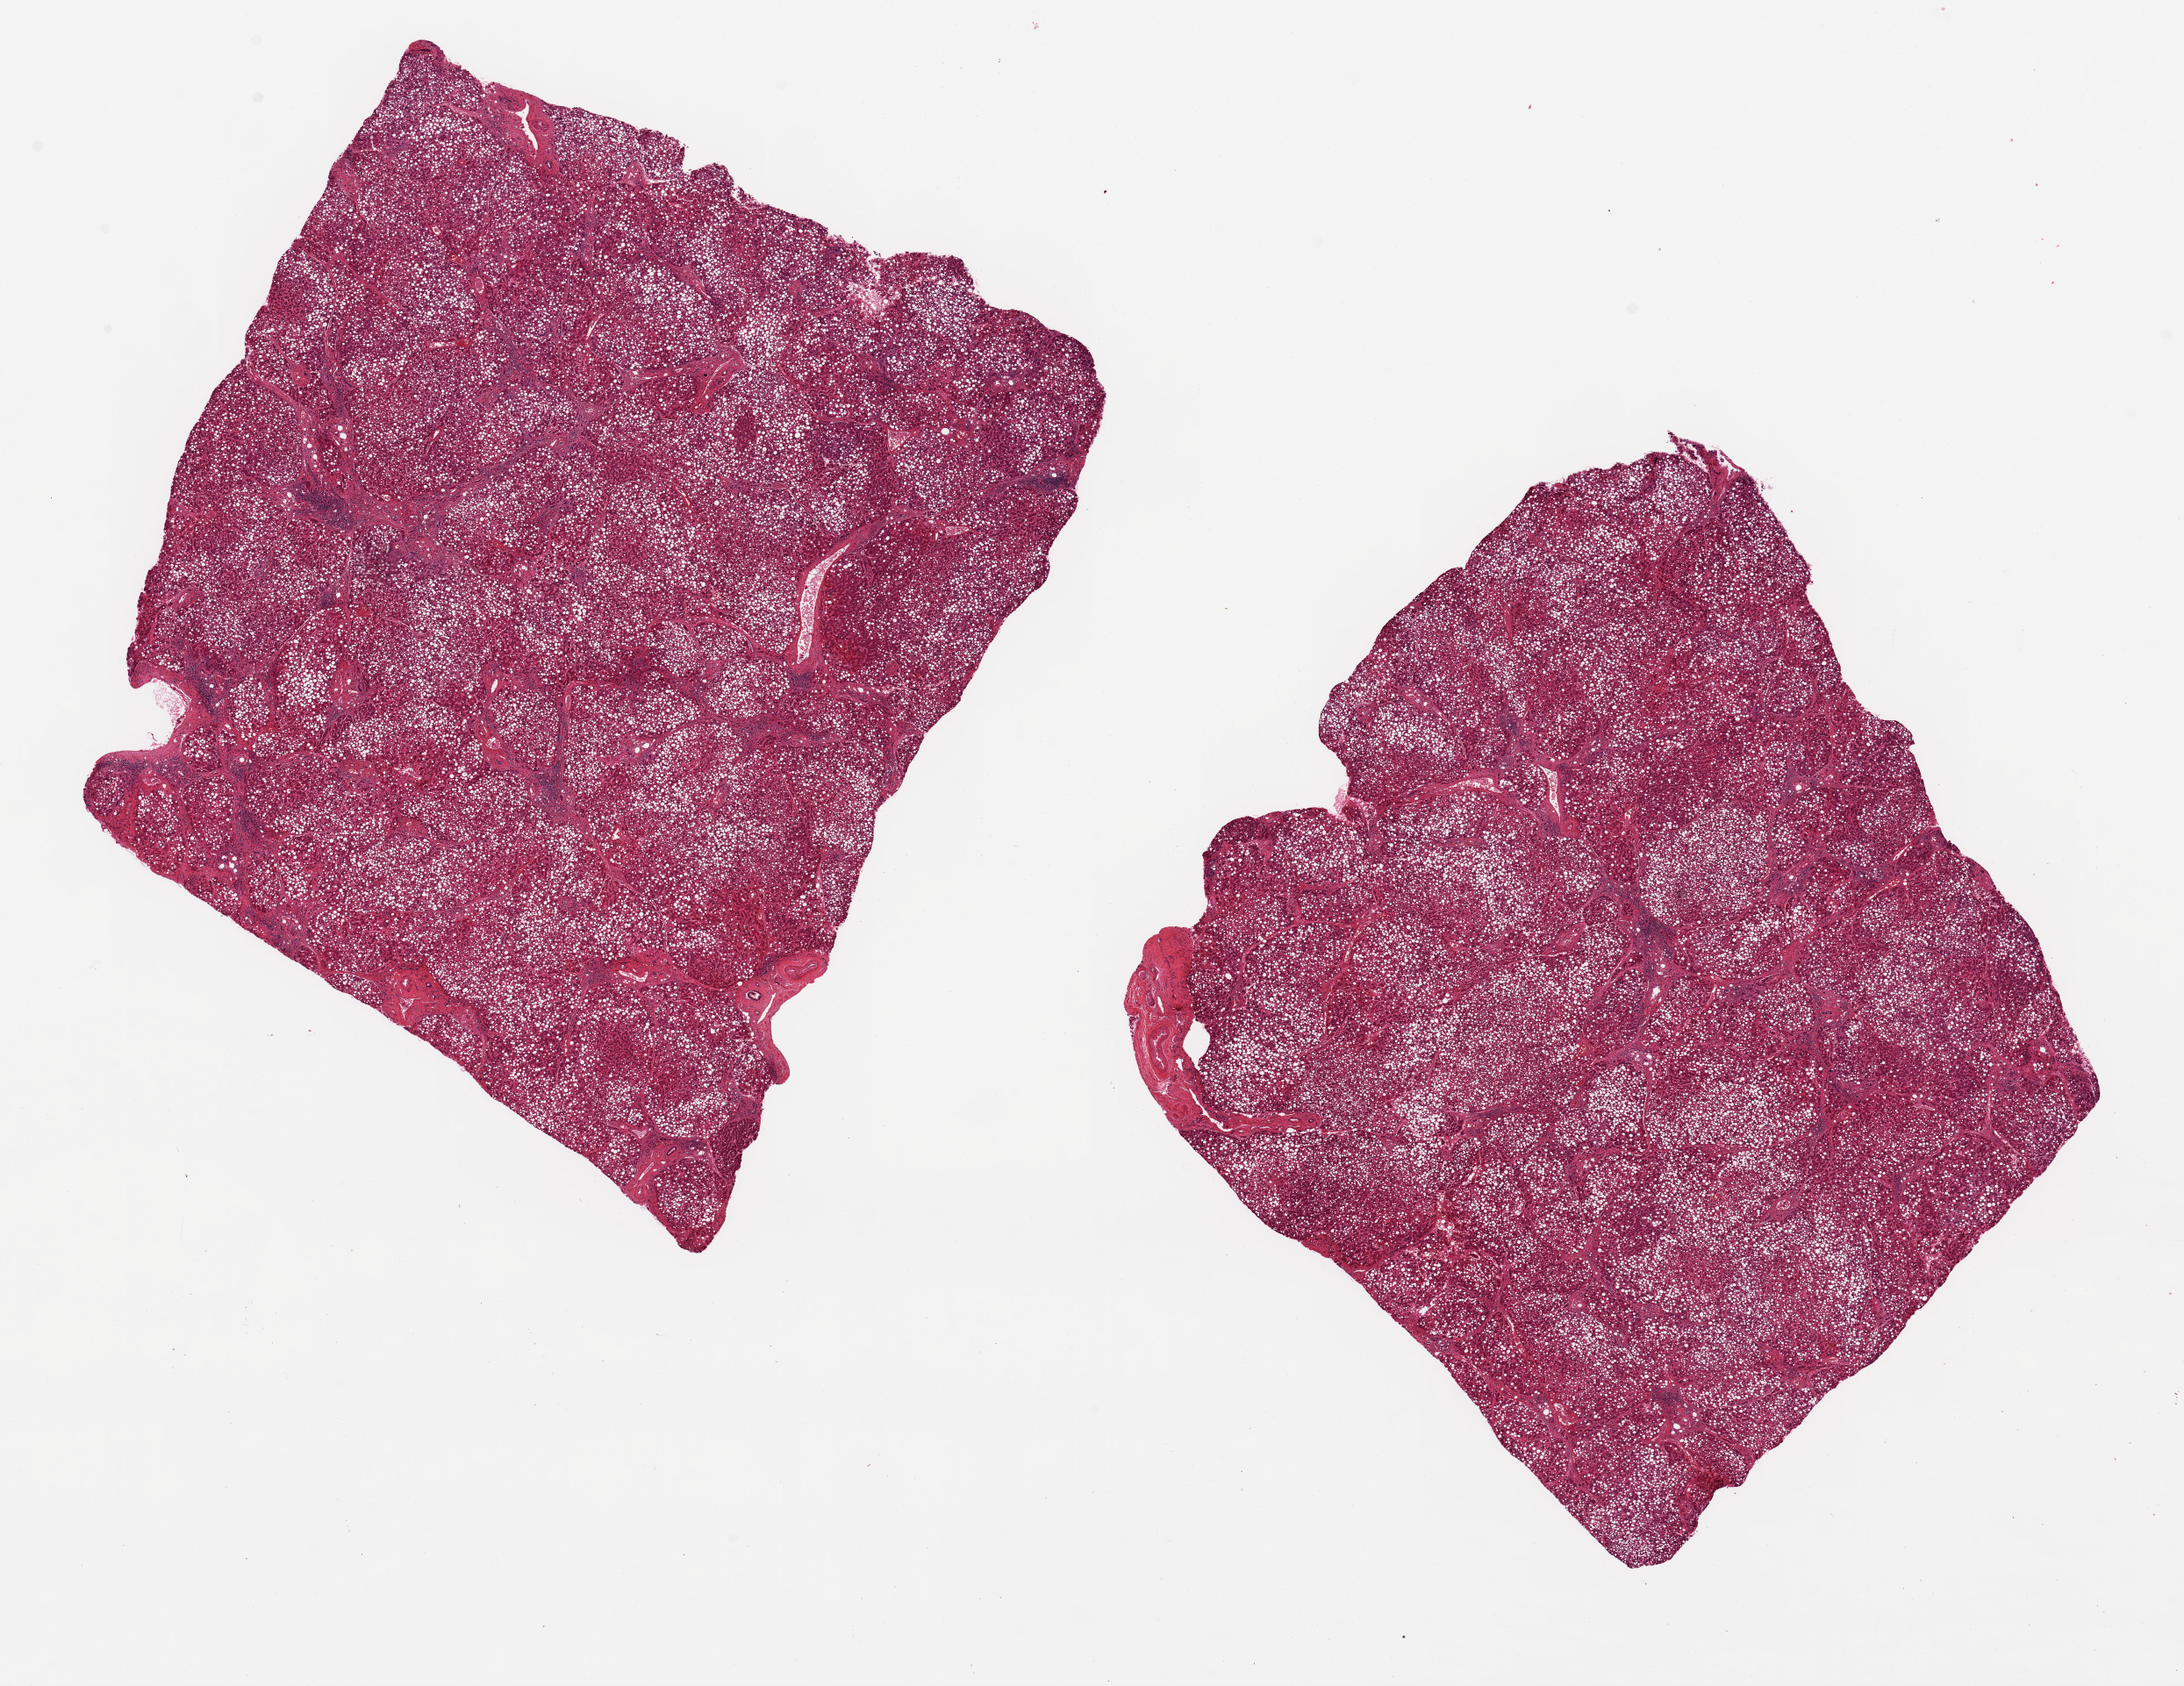
Digitized H&E-stained section — low-resolution overview of the scanned area, about 19.7 x 15.2 mm. PAXgene-fixed paraffin-embedded (PFPE) section. Sampled site (target tissue): liver. Donor tissue sample. Donor: male.
Pathologist's review note for this sample: 2 ~7.5x7.5mm aliquots, diffuse macrovesicular steatosis and chronic hepatitis with bridging fibrosis.